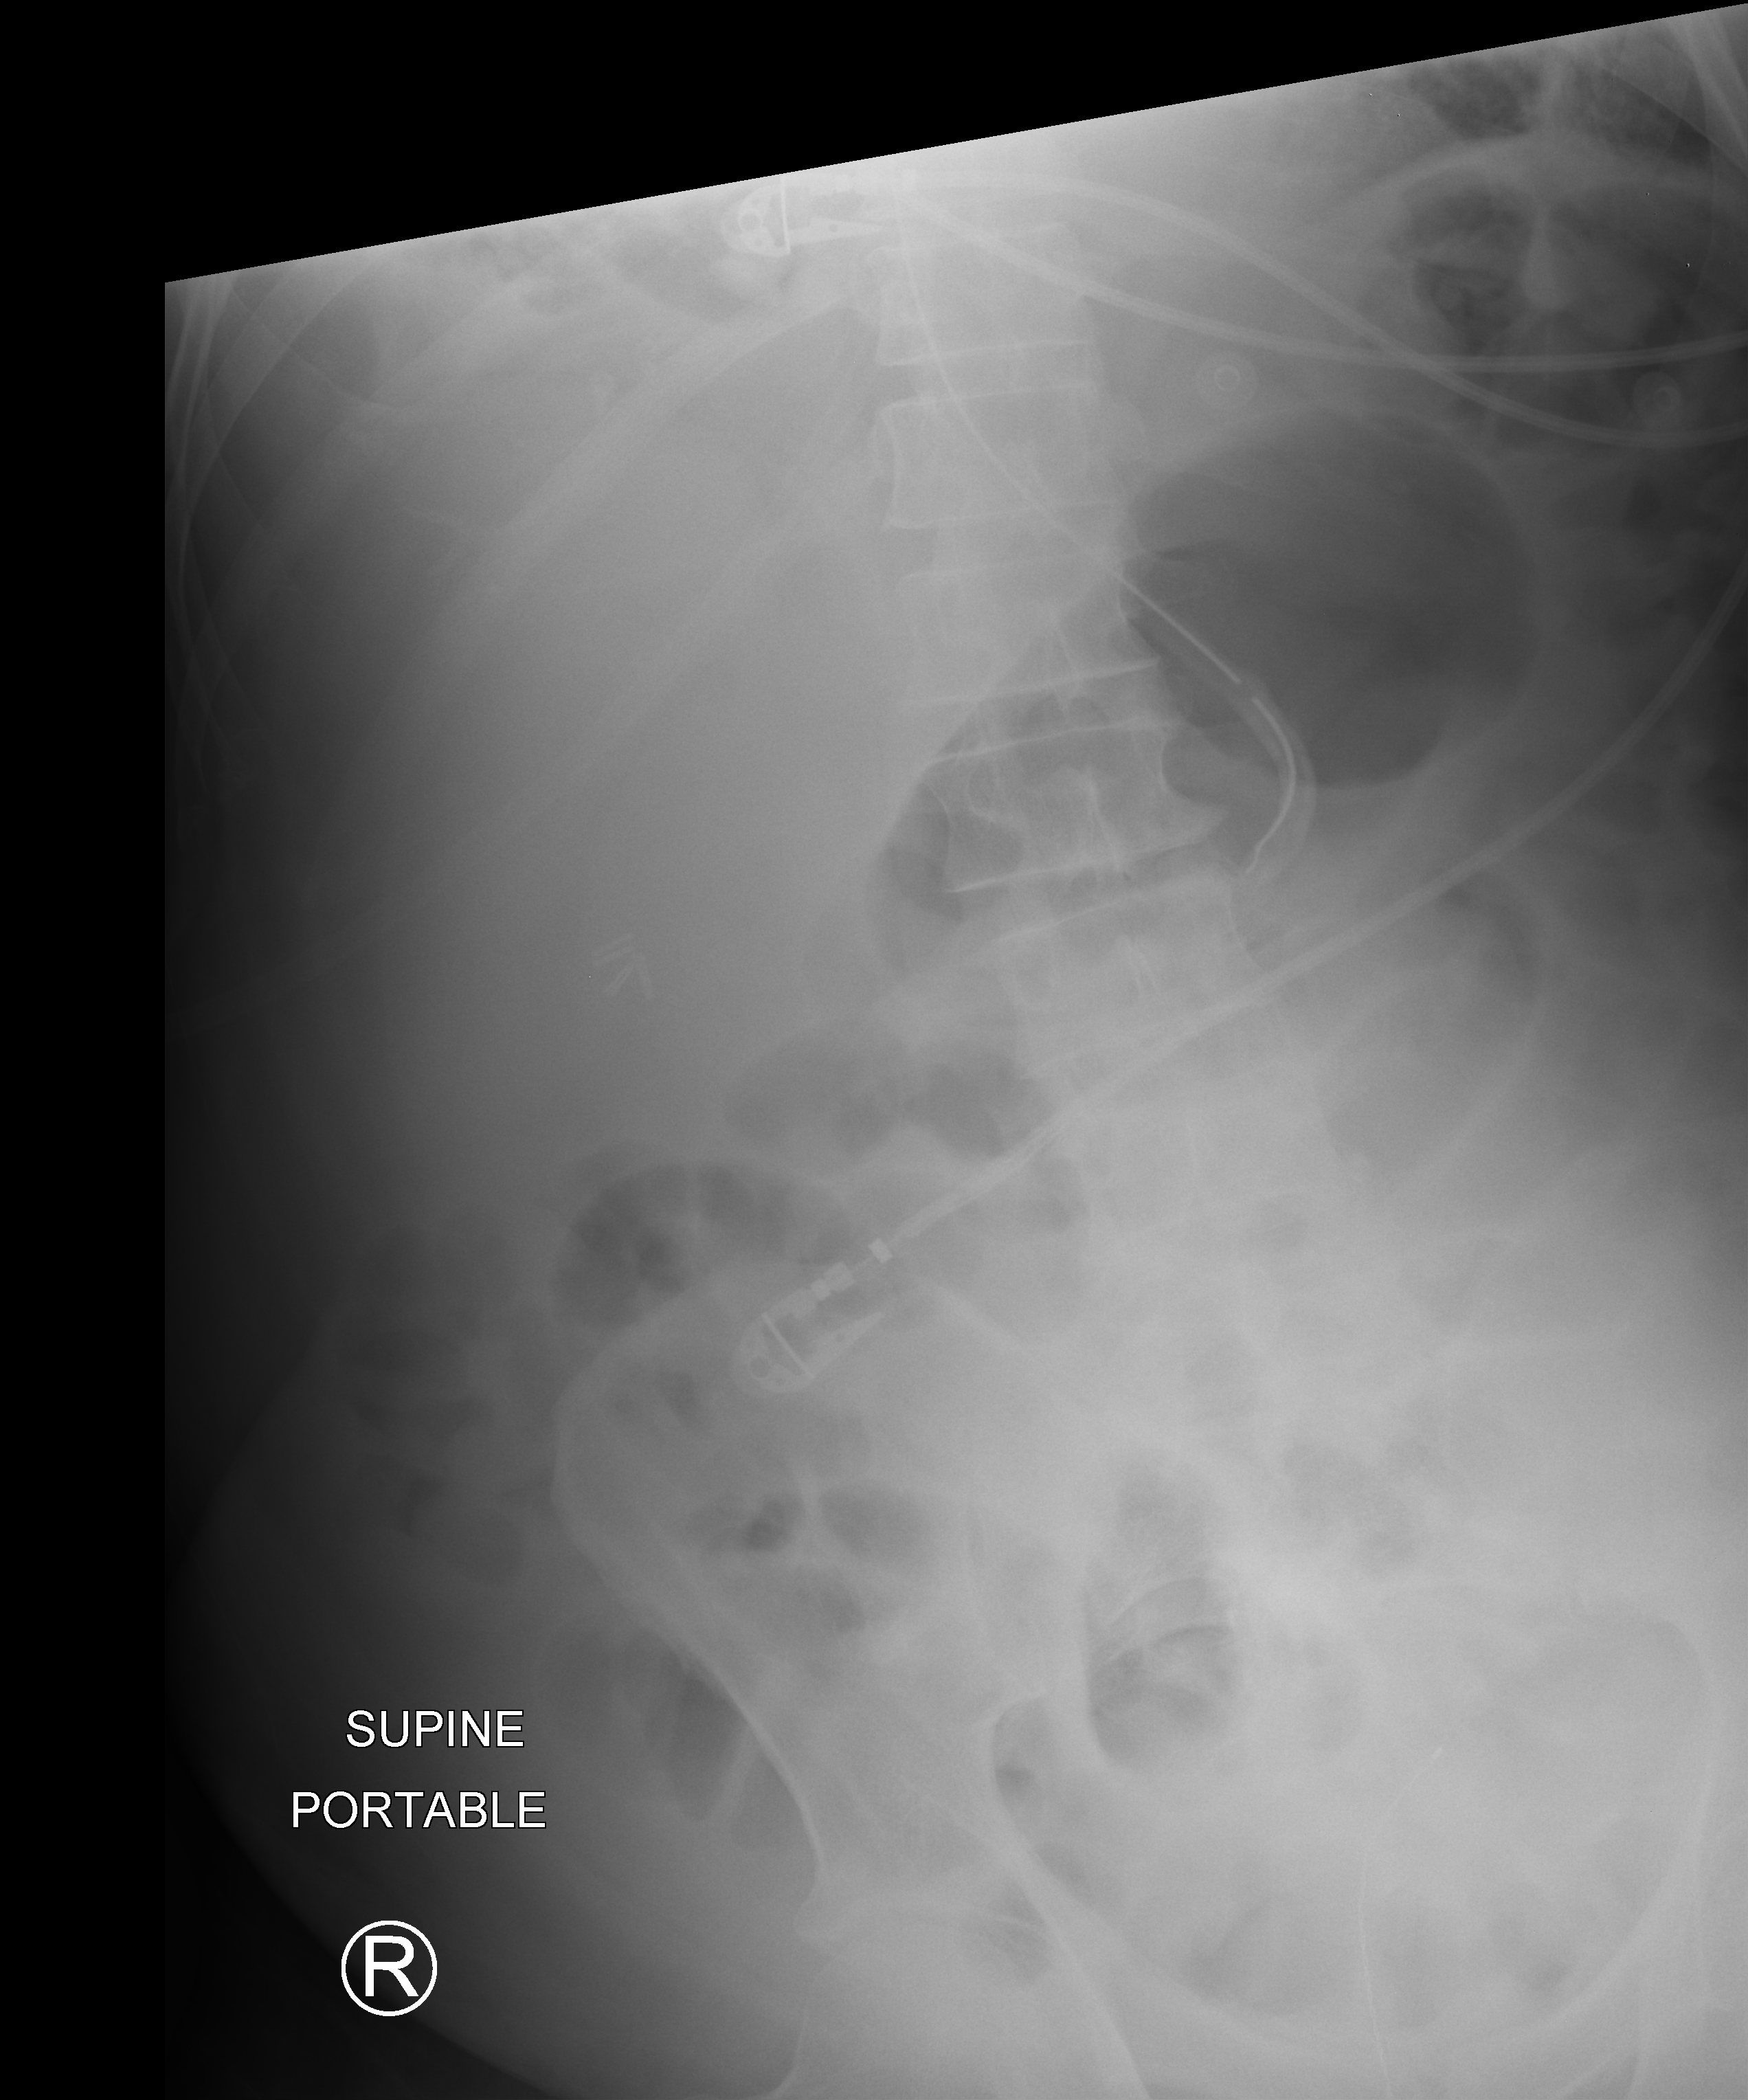
Bedside abdomen radiograph (computed radiography). Patient hospitalised with COVID-19; male, aged 75–90 years.
From the hospital-stay record, not from the radiograph (when in the stay this image was taken is not recorded):
- diabetes (admission record): no
- length of hospital stay: 70 days
- admitted to intensive care during this hospital stay: yes